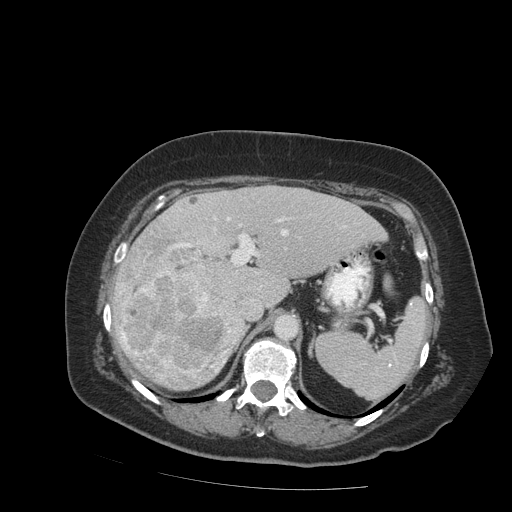
Contrast-enhanced abdominal CT (liver protocol), one axial slice. Slice 55 of 99 in the series (ordered by position). Reconstruction kernel STANDARD. 140 kVp. Soft-tissue window (W 400 / L 40 HU). 2.5 mm slice thickness. 512 × 512 image matrix, field of view 400 × 400 mm. From the clinical record (not read from this slice): diagnosis: hepatocellular carcinoma (patient treated with transarterial chemoembolisation; whether this scan precedes or follows treatment is not stated here); TNM stage (as recorded): Stage-IVB.
Structures marked on this image (semi-automatic segmentation, software-assisted and operator-edited):
- liver parenchyma outside the tumour (the mass and vessels are separate outlines, so this box may not span the whole liver): bounding box <112,186,387,390> (left, top, right, bottom; pixels)
- mass: <114,225,237,388>
- liver vessels: <182,217,345,301>